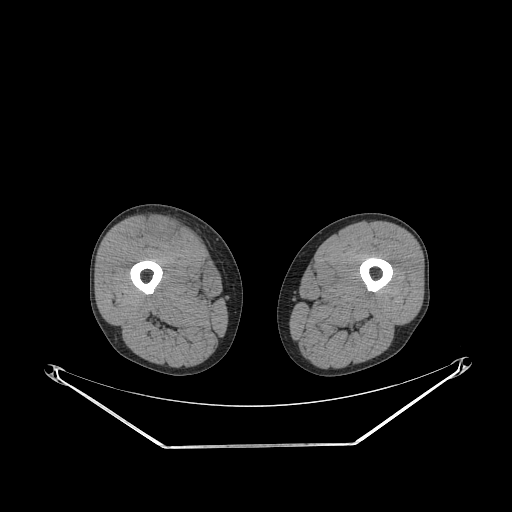
CT of an extremity soft-tissue mass (from a PET/CT study), one axial slice; slice 245 of 311 in the series (ordered by position); reconstruction kernel STANDARD; 140 kVp; soft-tissue window (W 400 / L 40 HU); 3.75 mm slice thickness; 512 × 512 image matrix, field of view 500 × 500 mm. Male patient. From the clinical record (not read from this slice): histological type: pleiomorphic leiomyosarcoma; grade: intermediate; site of the primary tumour: right thigh.
Outlined on this slice (expert contour drawn on MRI and transferred to this co-registered scan by the dataset authors):
- gross tumour volume including surrounding oedema: box from (x=148, y=217) to (x=181, y=241) px